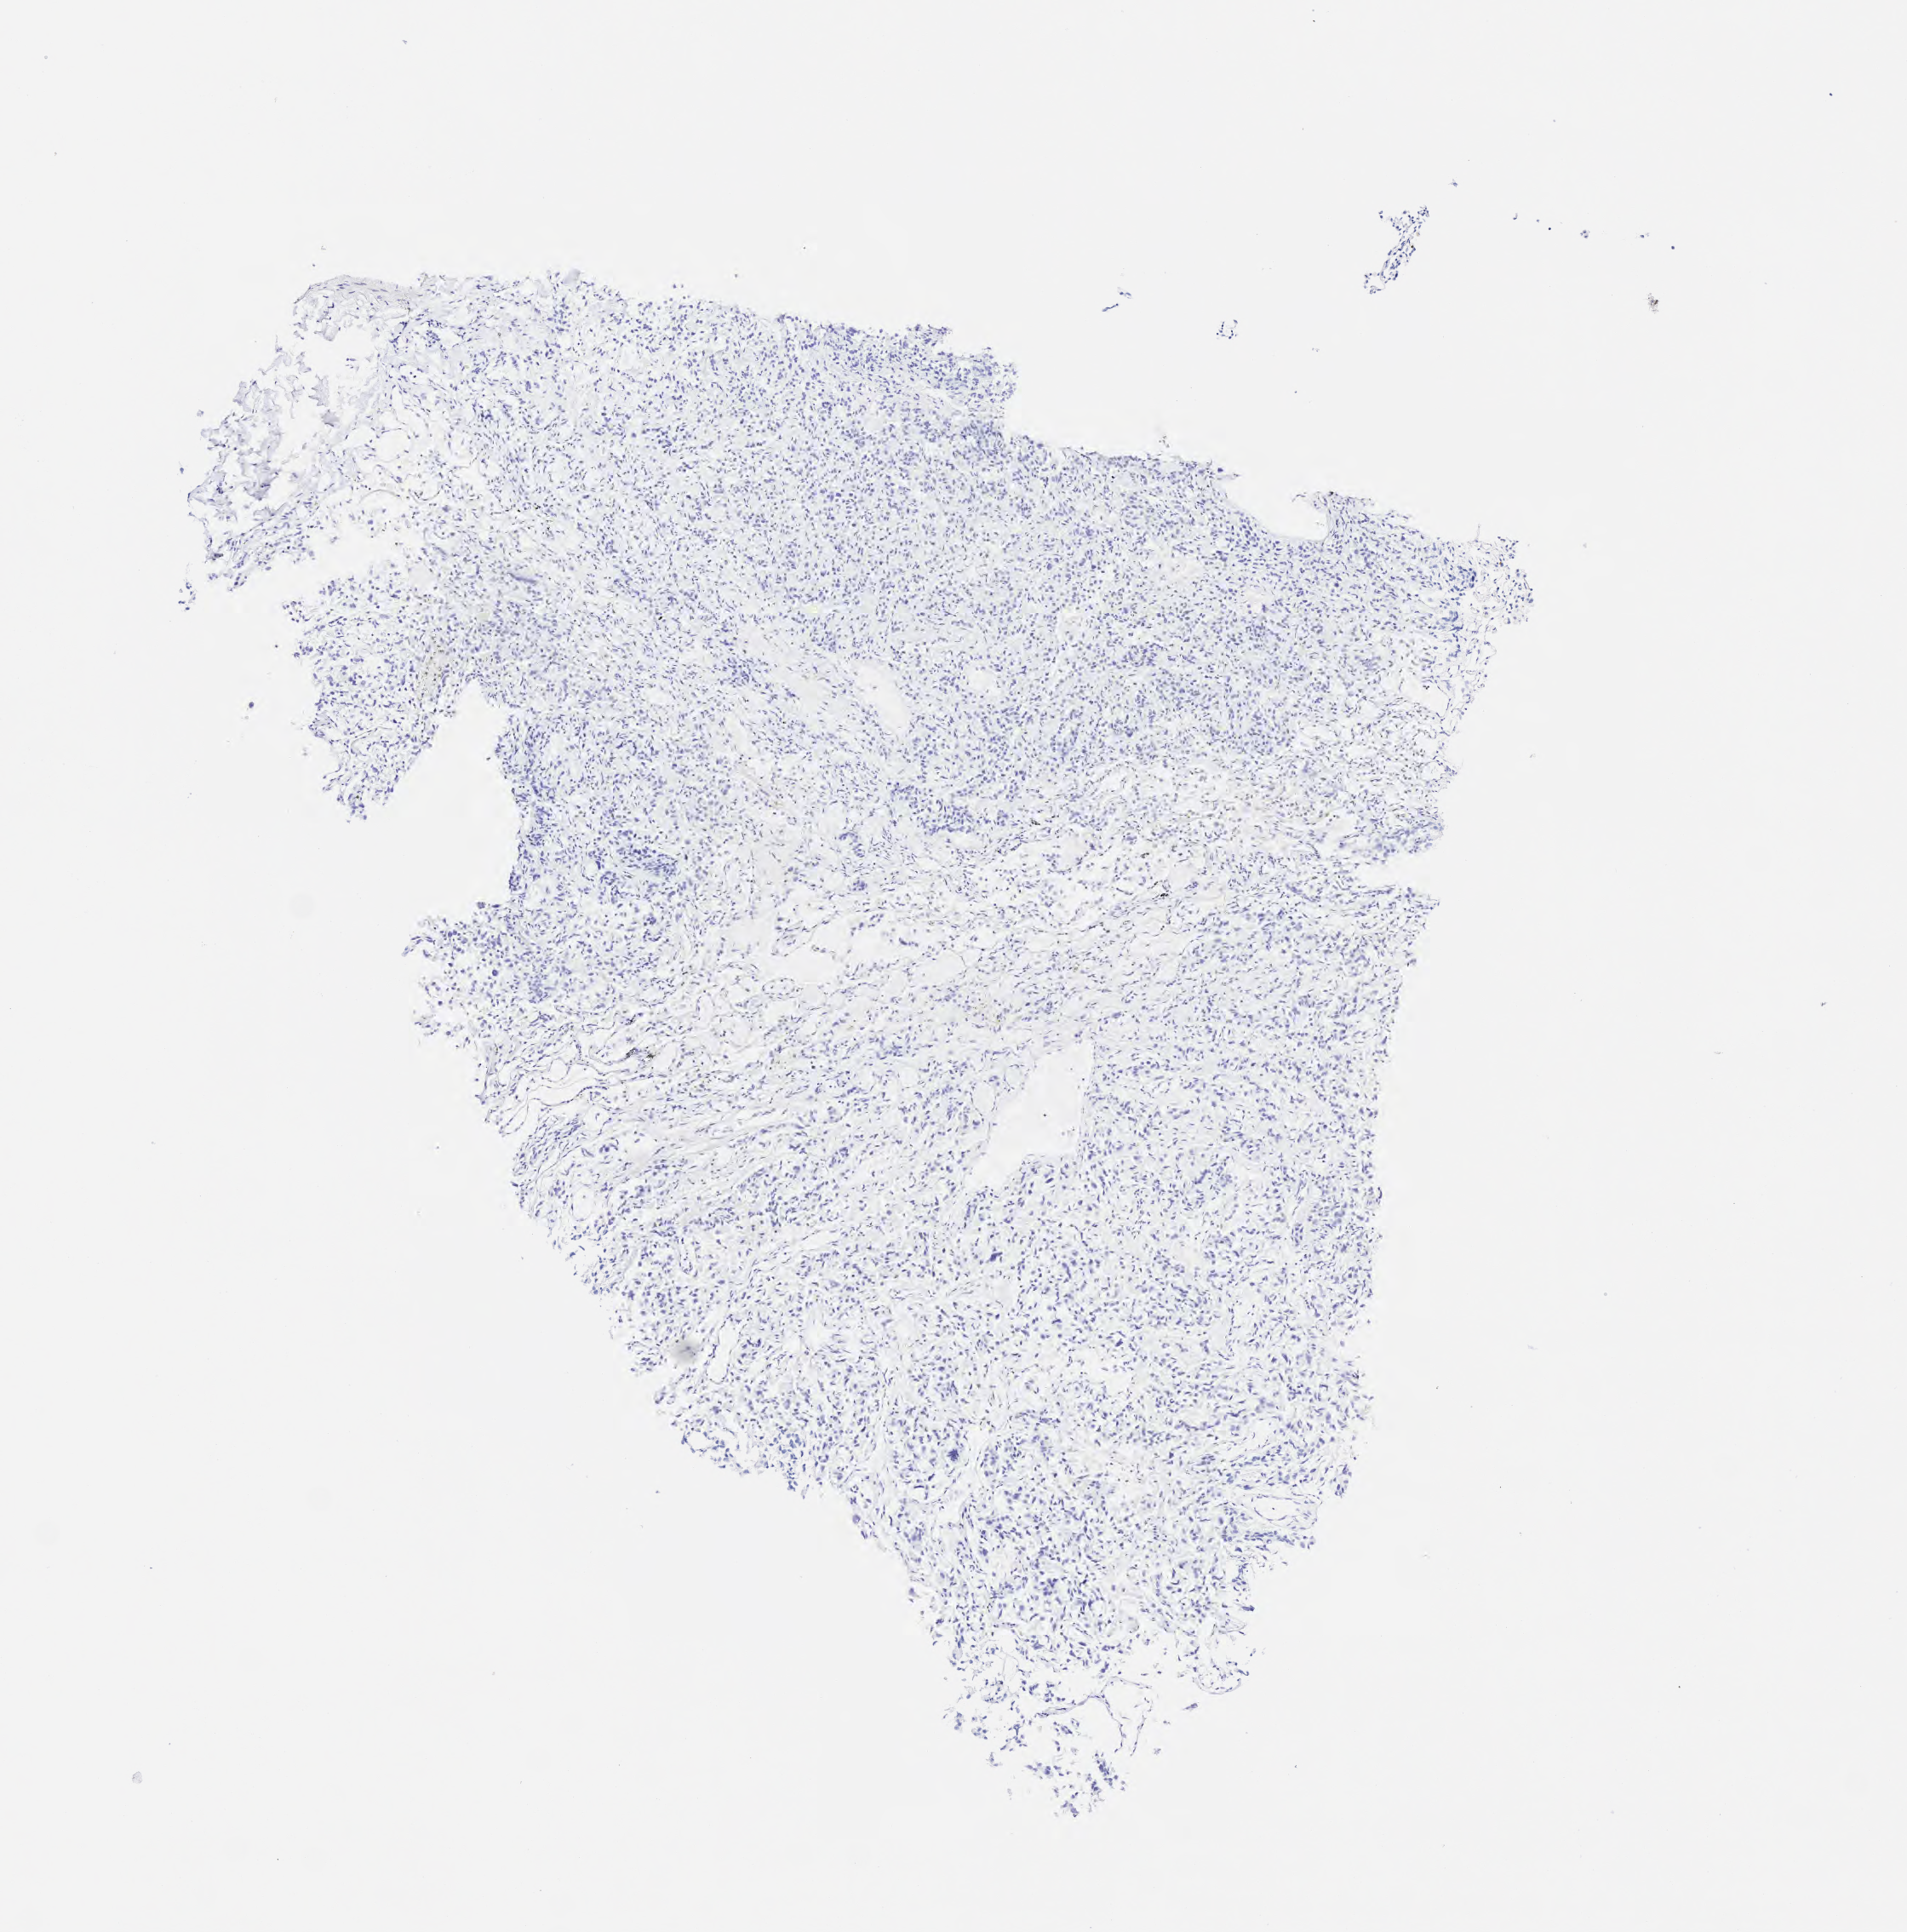
IHC for p40, whole-slide image, a low-resolution overview of the entire scanned area, about 4.5 x 4.6 mm, specimen: tumor tissue. Male patient.
• histologic diagnosis: Neoplasm, uncertain whether benign or malignant